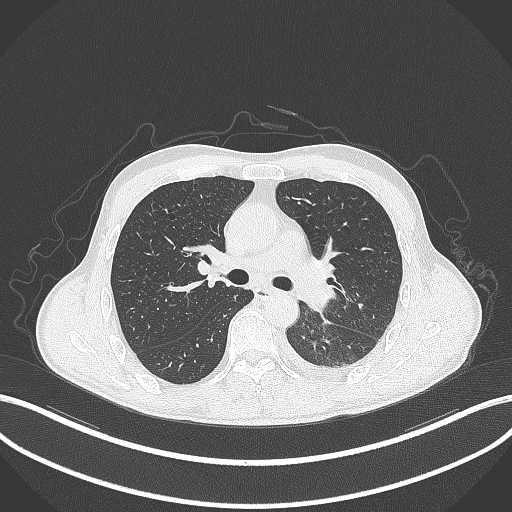
Chest CT, one axial slice. Position 203 of 295 along the scan axis. Reconstruction kernel B70f. Lung window (W 1500 / L -600 HU). 512 × 512 image matrix, field of view 400 × 400 mm. Male patient, age 47 years. Case-level facts recorded for this patient, not image findings: clinical TNM (as recorded): T3 N1 M1c; histopathological grade: G3.
Annotated regions visible in this slice (rectangle marked by the reading radiologist):
- lung tumour (recorded histology: small cell carcinoma): bounding box [x1, y1, x2, y2] px = [299, 275, 336, 312]